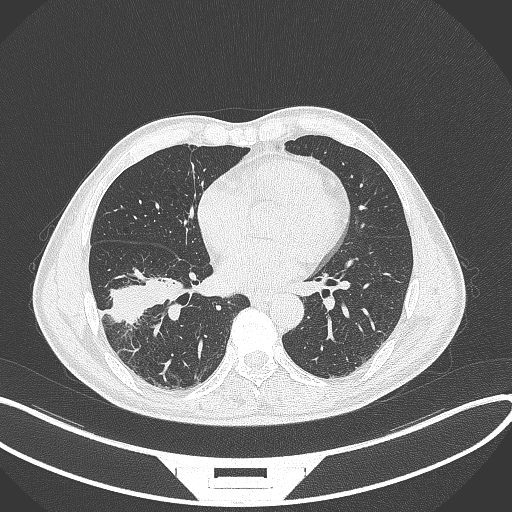
Chest CT, one axial slice. Slice 152 of 364 in the series (ordered by position). Reconstruction kernel B70f. Lung window (W 1500 / L -600 HU). 1 mm slice thickness. 512 × 512 image matrix, field of view 400 × 400 mm. Male patient, age 58 years. Case-level facts recorded for this patient, not image findings: clinical TNM (as recorded): T3 N0 M0; histopathological grade: G2.
Outlined on this slice (bounding box drawn by a radiologist):
- lung tumour (recorded histology: squamous cell carcinoma): box from (x=108, y=269) to (x=187, y=326) px